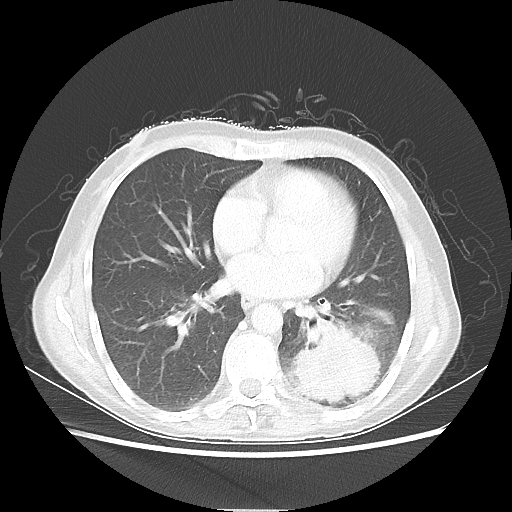
Chest CT, one axial slice. Position 25 of 56 along the scan axis. 80 kVp. Lung window (W 1500 / L -600 HU). 5 mm slice thickness. 512 × 512 image matrix, field of view 360 × 360 mm. Patient: female, 53 years. From the clinical record (not read from this slice): clinical TNM (as recorded): T3 N0 M0.
Annotated regions visible in this slice (bounding box drawn by a radiologist):
- lung tumour (recorded histology: adenocarcinoma): bounding box <290,319,381,402> (left, top, right, bottom; pixels)